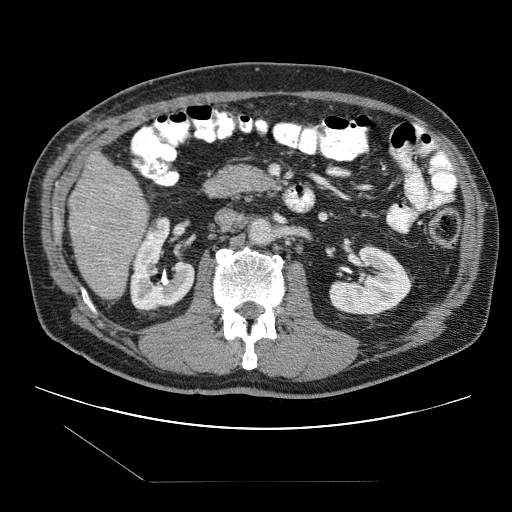
Contrast-enhanced abdominal CT (liver protocol), one axial slice. Position 30 of 109 along the scan axis. 120 kVp. One of 2 acquisitions stored at this slice position. Soft-tissue window (W 400 / L 40 HU). 2.5 mm slice thickness. 512 × 512 image matrix. From the clinical record (not read from this slice): diagnosis: hepatocellular carcinoma (patient treated with transarterial chemoembolisation; whether this scan precedes or follows treatment is not stated here); TNM stage (as recorded): Stage-IIIB; Child-Pugh class: A; tumour differentiation: well differentiated; tumour nodularity: multinodular.
Structures marked on this image (semi-automatic segmentation, software-assisted and operator-edited):
- liver parenchyma outside the tumour (the mass and vessels are separate outlines, so this box may not span the whole liver): bounding box <68,152,149,298> (left, top, right, bottom; pixels)
- liver vessels: <91,226,95,229>